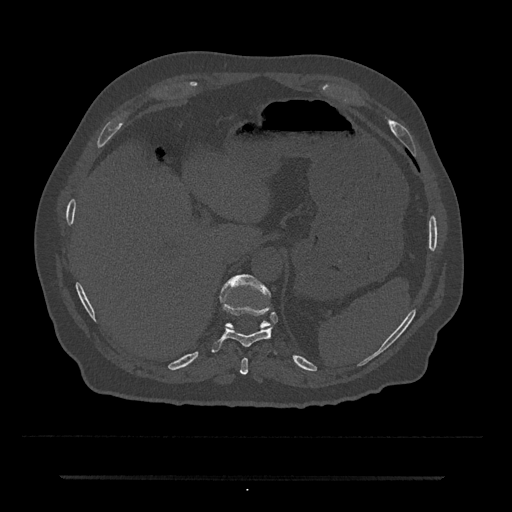
CT including the spine, one axial slice; position 222 of 797 along the scan axis; 120 kVp; bone window (W 1800 / L 400 HU); 0.5 mm slice thickness; 512 × 512 image matrix, field of view 437 × 437 mm. Patient: male, 69 years. From the clinical record (not read from this slice): primary cancer: prostate.
Outlined on this slice (semi-automatically segmented with operator editing):
- T10 vertebra: box from (x=211, y=304) to (x=277, y=354) px
- T11 vertebra: (x=220, y=274)–(x=271, y=329)
- T9 vertebra: (x=240, y=357)–(x=248, y=375)